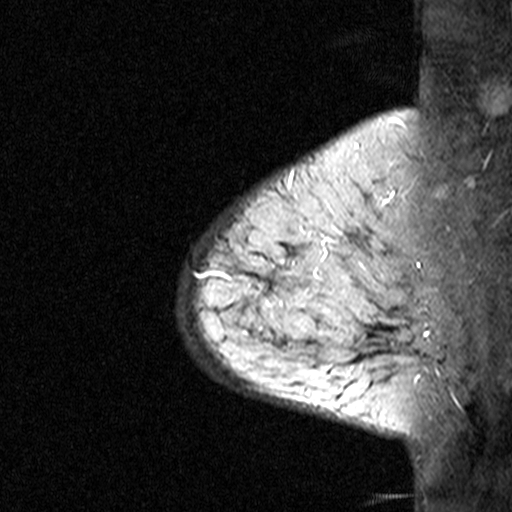
Breast MRI (dynamic contrast-enhanced), one sagittal slice. Slice 35 of 44 in the series (ordered by position). Dynamic contrast-enhanced study with each time point stored as its own series, time point 3 of 4 at this slice position (ordered by acquisition time). 1.5 T. TE 4.5 ms, TR 11 ms. 512 × 512 image matrix, field of view 200 × 200 mm. Patient: female, 65 years. From the clinical record (not read from this slice): setting: breast cancer imaged before/during neoadjuvant chemotherapy; receptor status: HER2-positive.
Outlined on this slice (semi-automatic segmentation, software-assisted and operator-edited):
- analysis volume of interest (the breast-tissue region the enhancement analysis was run in; not a lesion): bounding box <182,190,353,361> (left, top, right, bottom; pixels)
- tumour enhancement mask (voxels above the 90 % enhancement threshold inside the analysis volume of interest): <193,260,288,292>